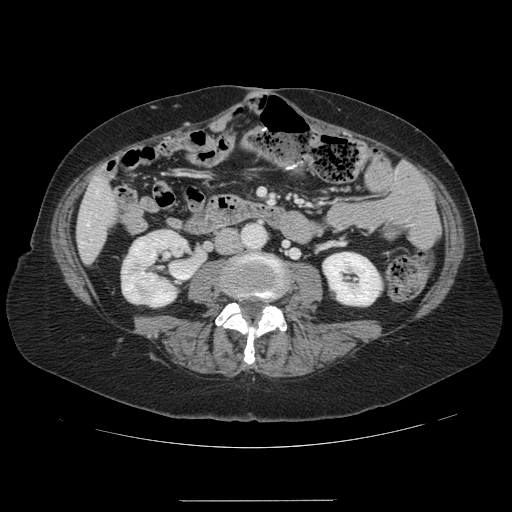
Contrast-enhanced abdominal CT, one axial slice. Intravenous contrast given. Soft-tissue window (W 400 / L 40 HU). 2.5 mm slice thickness. 512 × 512 image matrix, field of view 393 × 393 mm. Female patient, age 74 years. Case-level facts recorded for this patient, not image findings: diagnosis: colorectal cancer liver metastases, imaged before liver resection; multiple liver metastases: yes.
Outlined on this slice (manually delineated by an expert):
- hepatic veins: bounding box <87,223,89,225> (left, top, right, bottom; pixels)
- liver: <77,179,115,262>
- planned liver remnant (the part of the liver to remain after resection): <77,199,93,262>